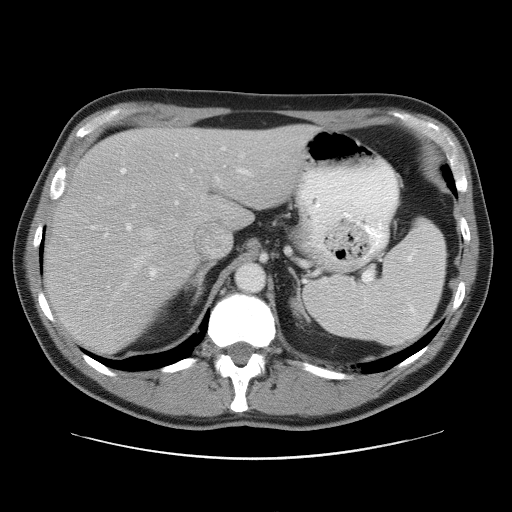
Contrast-enhanced abdominal CT, one axial slice. Slice 40 of 52 in the series (ordered by position). Reconstruction kernel STANDARD. 120 kVp. Intravenous contrast given. Soft-tissue window (W 400 / L 40 HU). 5 mm slice thickness. 512 × 512 image matrix, field of view 393 × 393 mm. Male patient, age 70 years. Case-level facts recorded for this patient, not image findings: diagnosis: colorectal cancer liver metastases, imaged before liver resection; multiple liver metastases: yes; largest metastasis: 4 cm; disease in both lobes: yes.
Structures marked on this image (expert manual segmentation):
- hepatic veins: bounding box [x1, y1, x2, y2] px = [133, 152, 245, 269]
- liver: [46, 126, 313, 356]
- planned liver remnant (the part of the liver to remain after resection): [108, 126, 312, 214]
- portal vein (with intrahepatic branches): [121, 147, 252, 284]